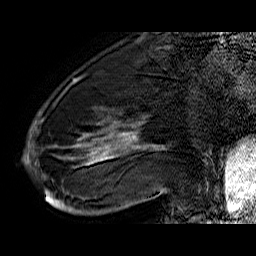
Breast MRI (dynamic contrast-enhanced), one sagittal slice; position 18 of 60 along the scan axis; dynamic contrast-enhanced series, time point 2 of 6 at this slice position (early post-contrast); 1.5 T; TE 6.4 ms, TR 32.9 ms; 4 mm slice thickness; 256 × 256 image matrix, field of view 200 × 200 mm. Female patient. From the clinical record (not read from this slice): setting: breast cancer imaged before/during neoadjuvant chemotherapy; receptor status: HR-positive, HER2-negative.
Outlined on this slice (semi-automatically segmented with operator editing):
- analysis volume of interest (the breast-tissue region the enhancement analysis was run in; not a lesion): bounding box (x1, y1, x2, y2) in pixels: (45, 74, 176, 210)
- tumour enhancement mask (voxels above the 100 % enhancement threshold inside the analysis volume of interest): (45, 123, 164, 207)